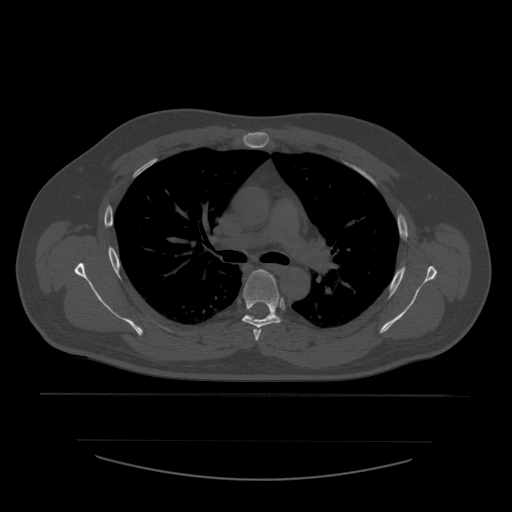
CT including the spine, one axial slice. Position 400 of 532 along the scan axis. 120 kVp. Bone window (W 1800 / L 400 HU). 512 × 512 image matrix. Patient age 44 years. From the clinical record (not read from this slice): primary cancer: soft tissue sarcoma.
Structures marked on this image (semi-automatic segmentation, software-assisted and operator-edited):
- T4 vertebra: box from (x=253, y=325) to (x=266, y=341) px
- T5 vertebra: (x=242, y=270)–(x=281, y=328)